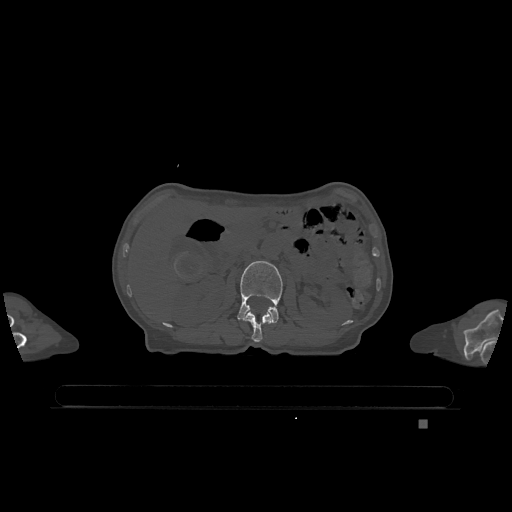
CT including the spine, one axial slice; slice 438 of 1317 in the series (ordered by position); bone window (W 1800 / L 400 HU); 0.5 mm slice thickness; 512 × 512 image matrix. Female patient, age 74 years. From the clinical record (not read from this slice): primary cancer: lung; vertebrae with lytic lesions (as recorded): T1, T4, T5, T6, L4, L5.
Annotated regions visible in this slice (semi-automatically segmented with operator editing):
- L1 vertebra: bounding box <245,310,272,342> (left, top, right, bottom; pixels)
- L2 vertebra: <238,261,283,323>